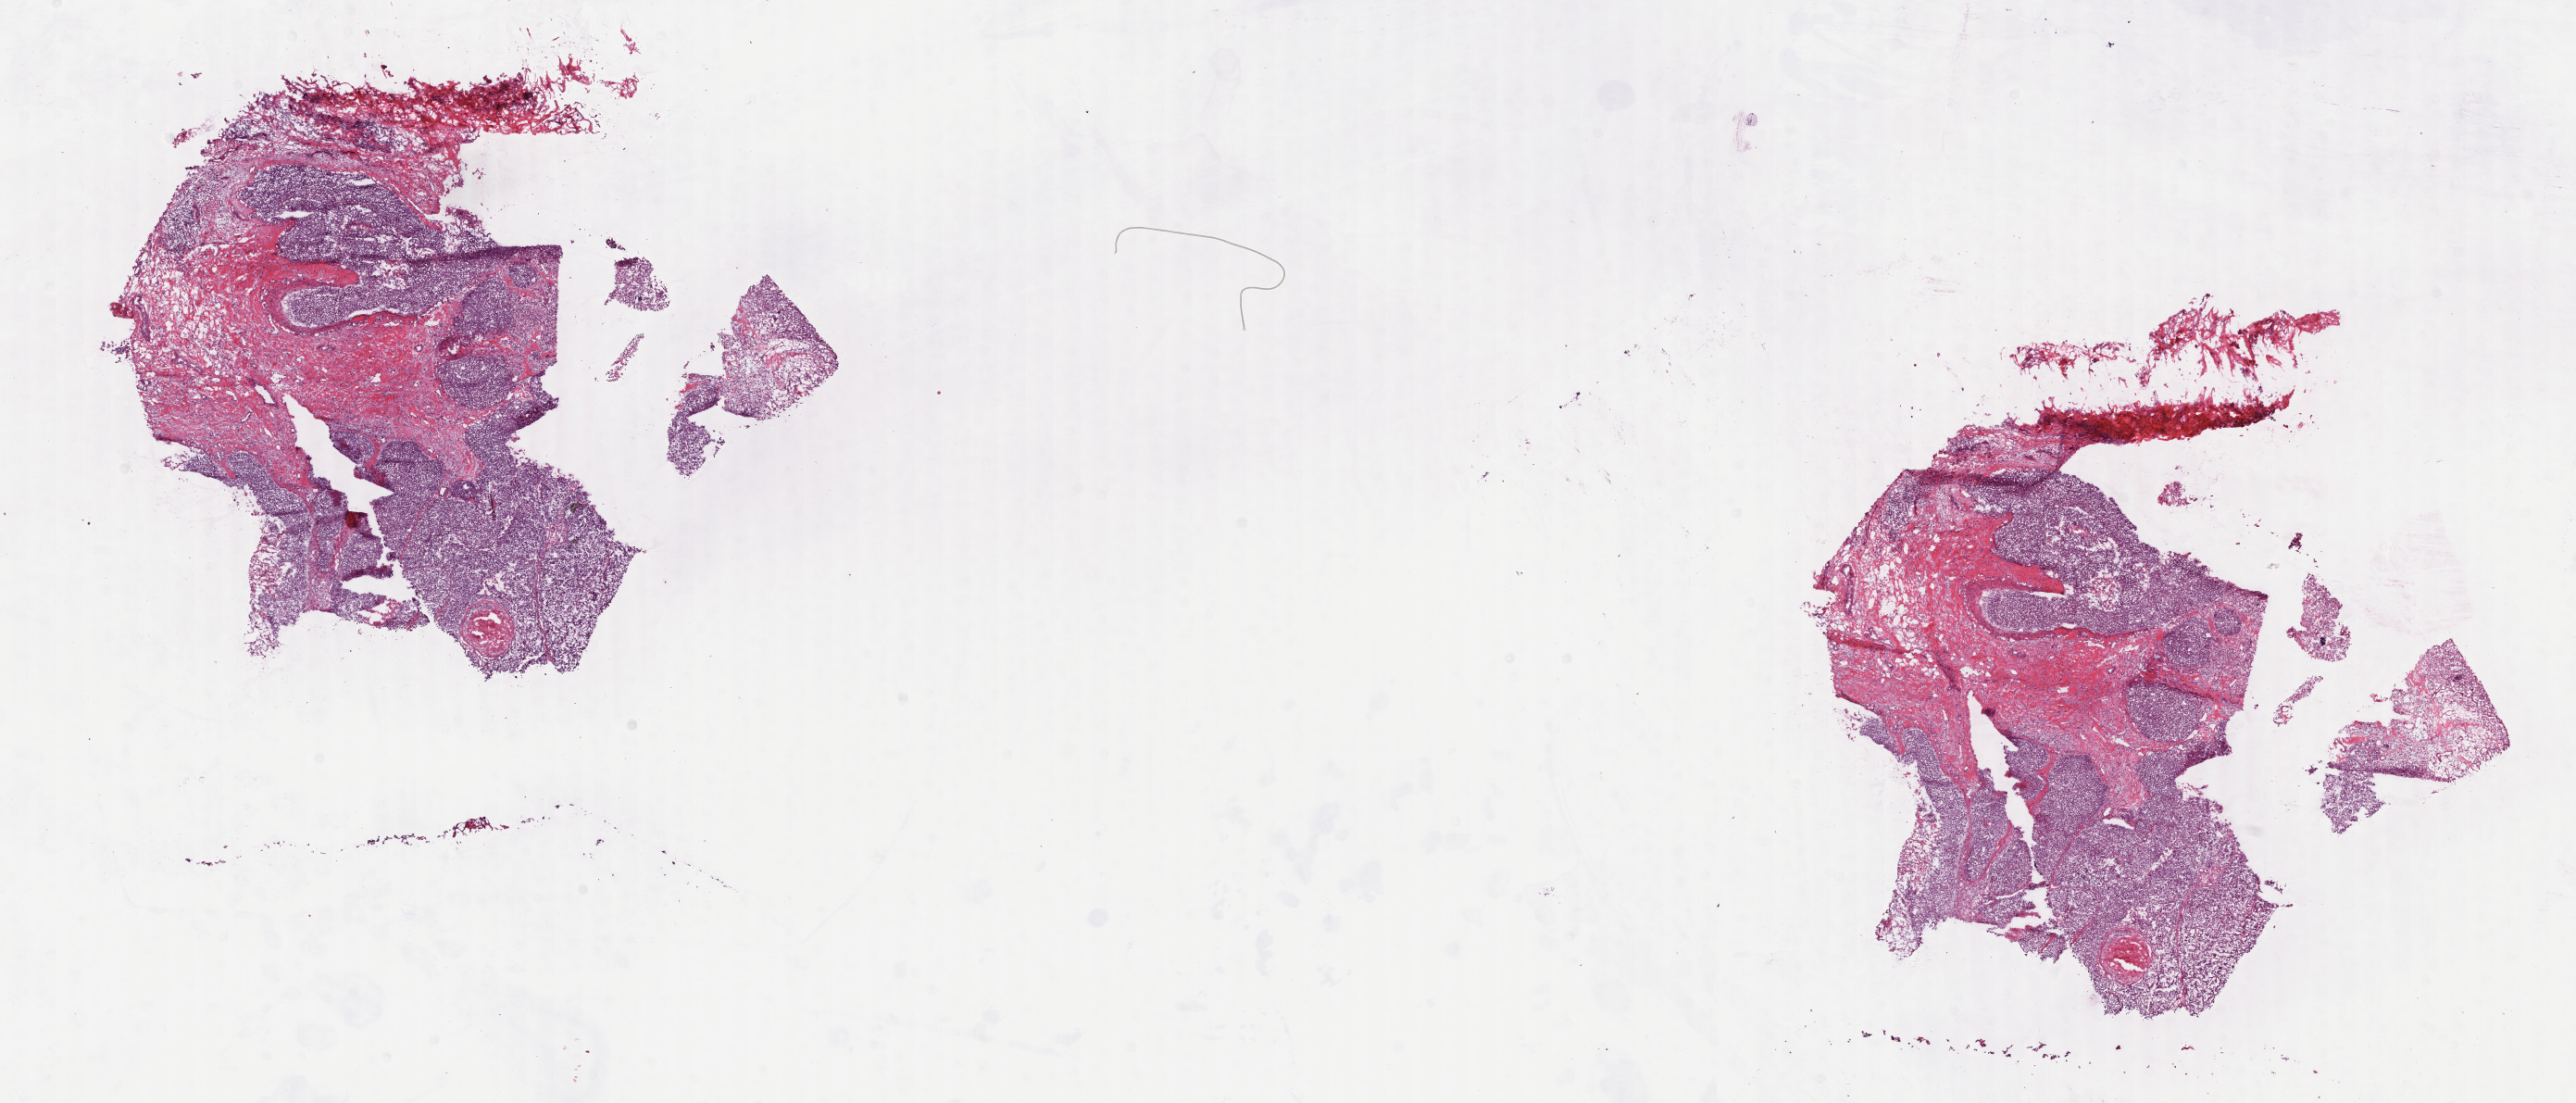
H&E whole-slide image, shown as a low-resolution overview of the whole scanned area (about 22.1 x 9.5 mm); frozen section; primary tumour sample from the breast. Patient: female, age at initial diagnosis 45 years.
Pathologic diagnosis: Infiltrating duct carcinoma, NOS.